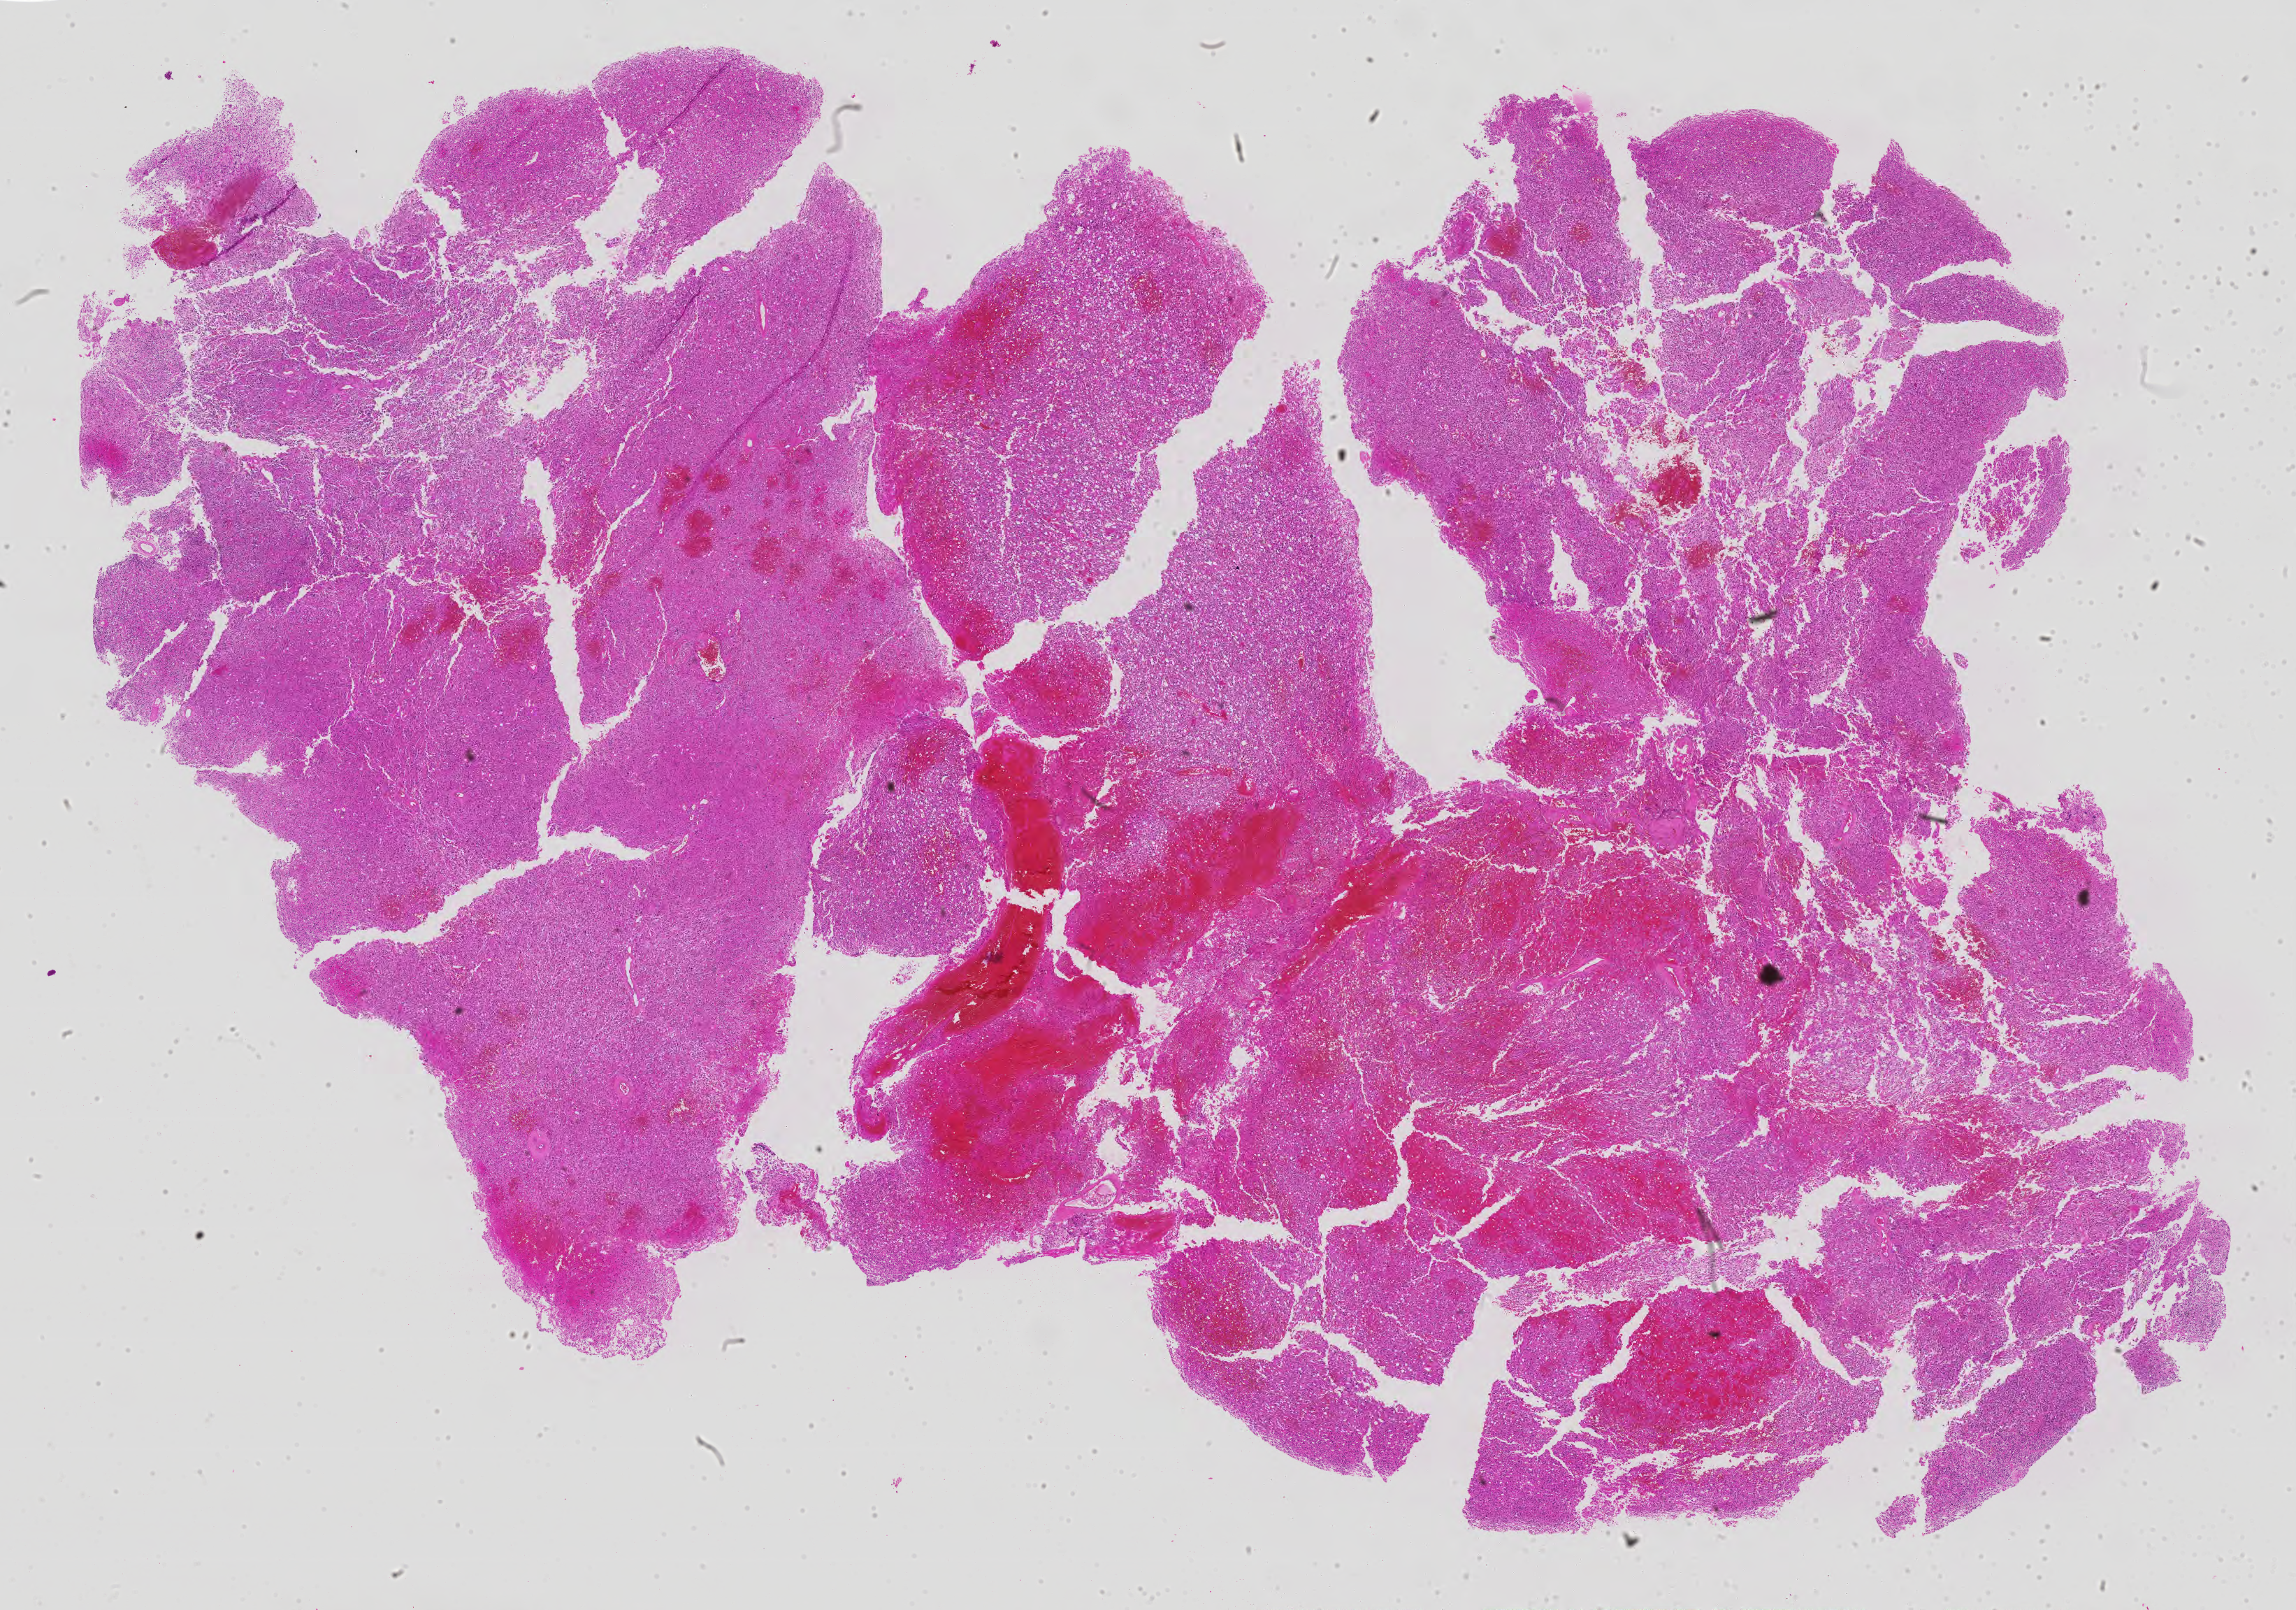
Digitized Hematoxylin and eosin (H&E) stained tissue section (whole slide), whole scanned area (about 26.3 x 18.4 mm, acquisition: 40x scan) shown as a low-resolution overview, FFPE section, sample: primary tumour, brain. Female, age 26 years at initial diagnosis. Histologic grade: G3 (poorly differentiated).
• histologic diagnosis: Mixed glioma (cerebrum)